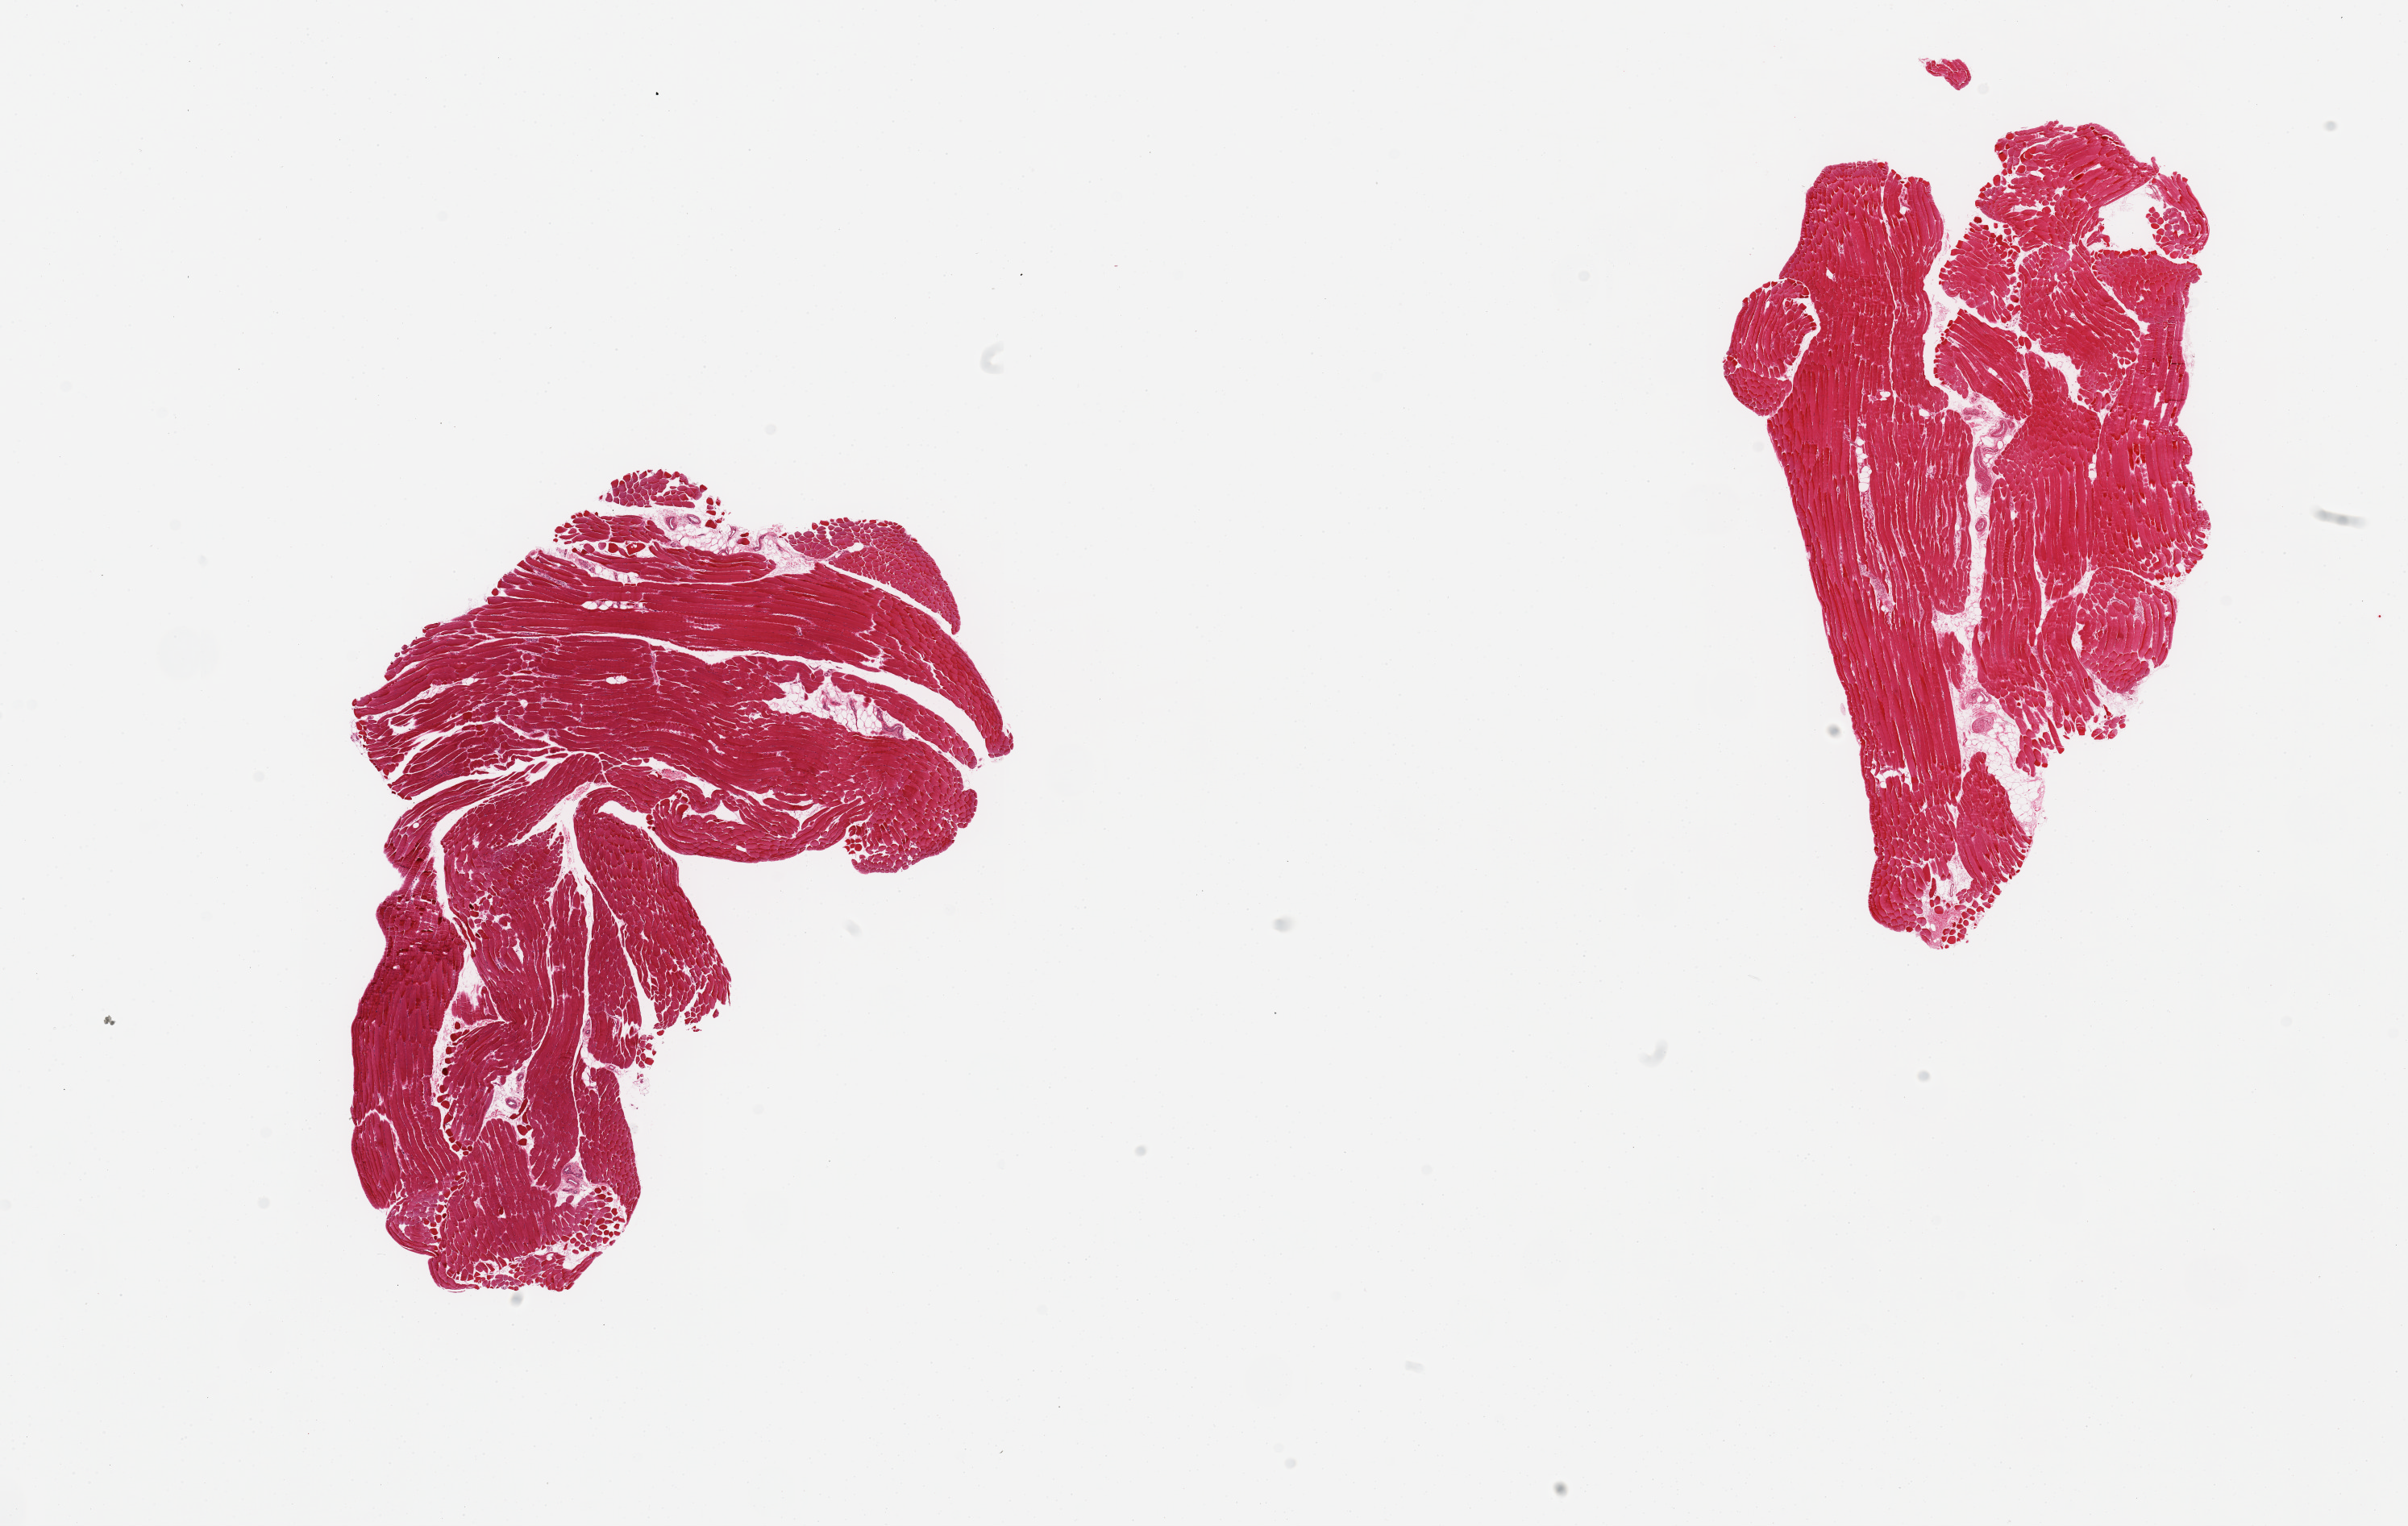
Digitized haematoxylin and eosin-stained section — a low-resolution overview of the entire scanned area, about 23.6 x 15.0 mm (acquisition: 20x scan), PAXgene-fixed paraffin-embedded (PFPE) section, section of skeletal muscle (target tissue), donor tissue sample.
* reviewer comment on this tissue sample: 2 pieces